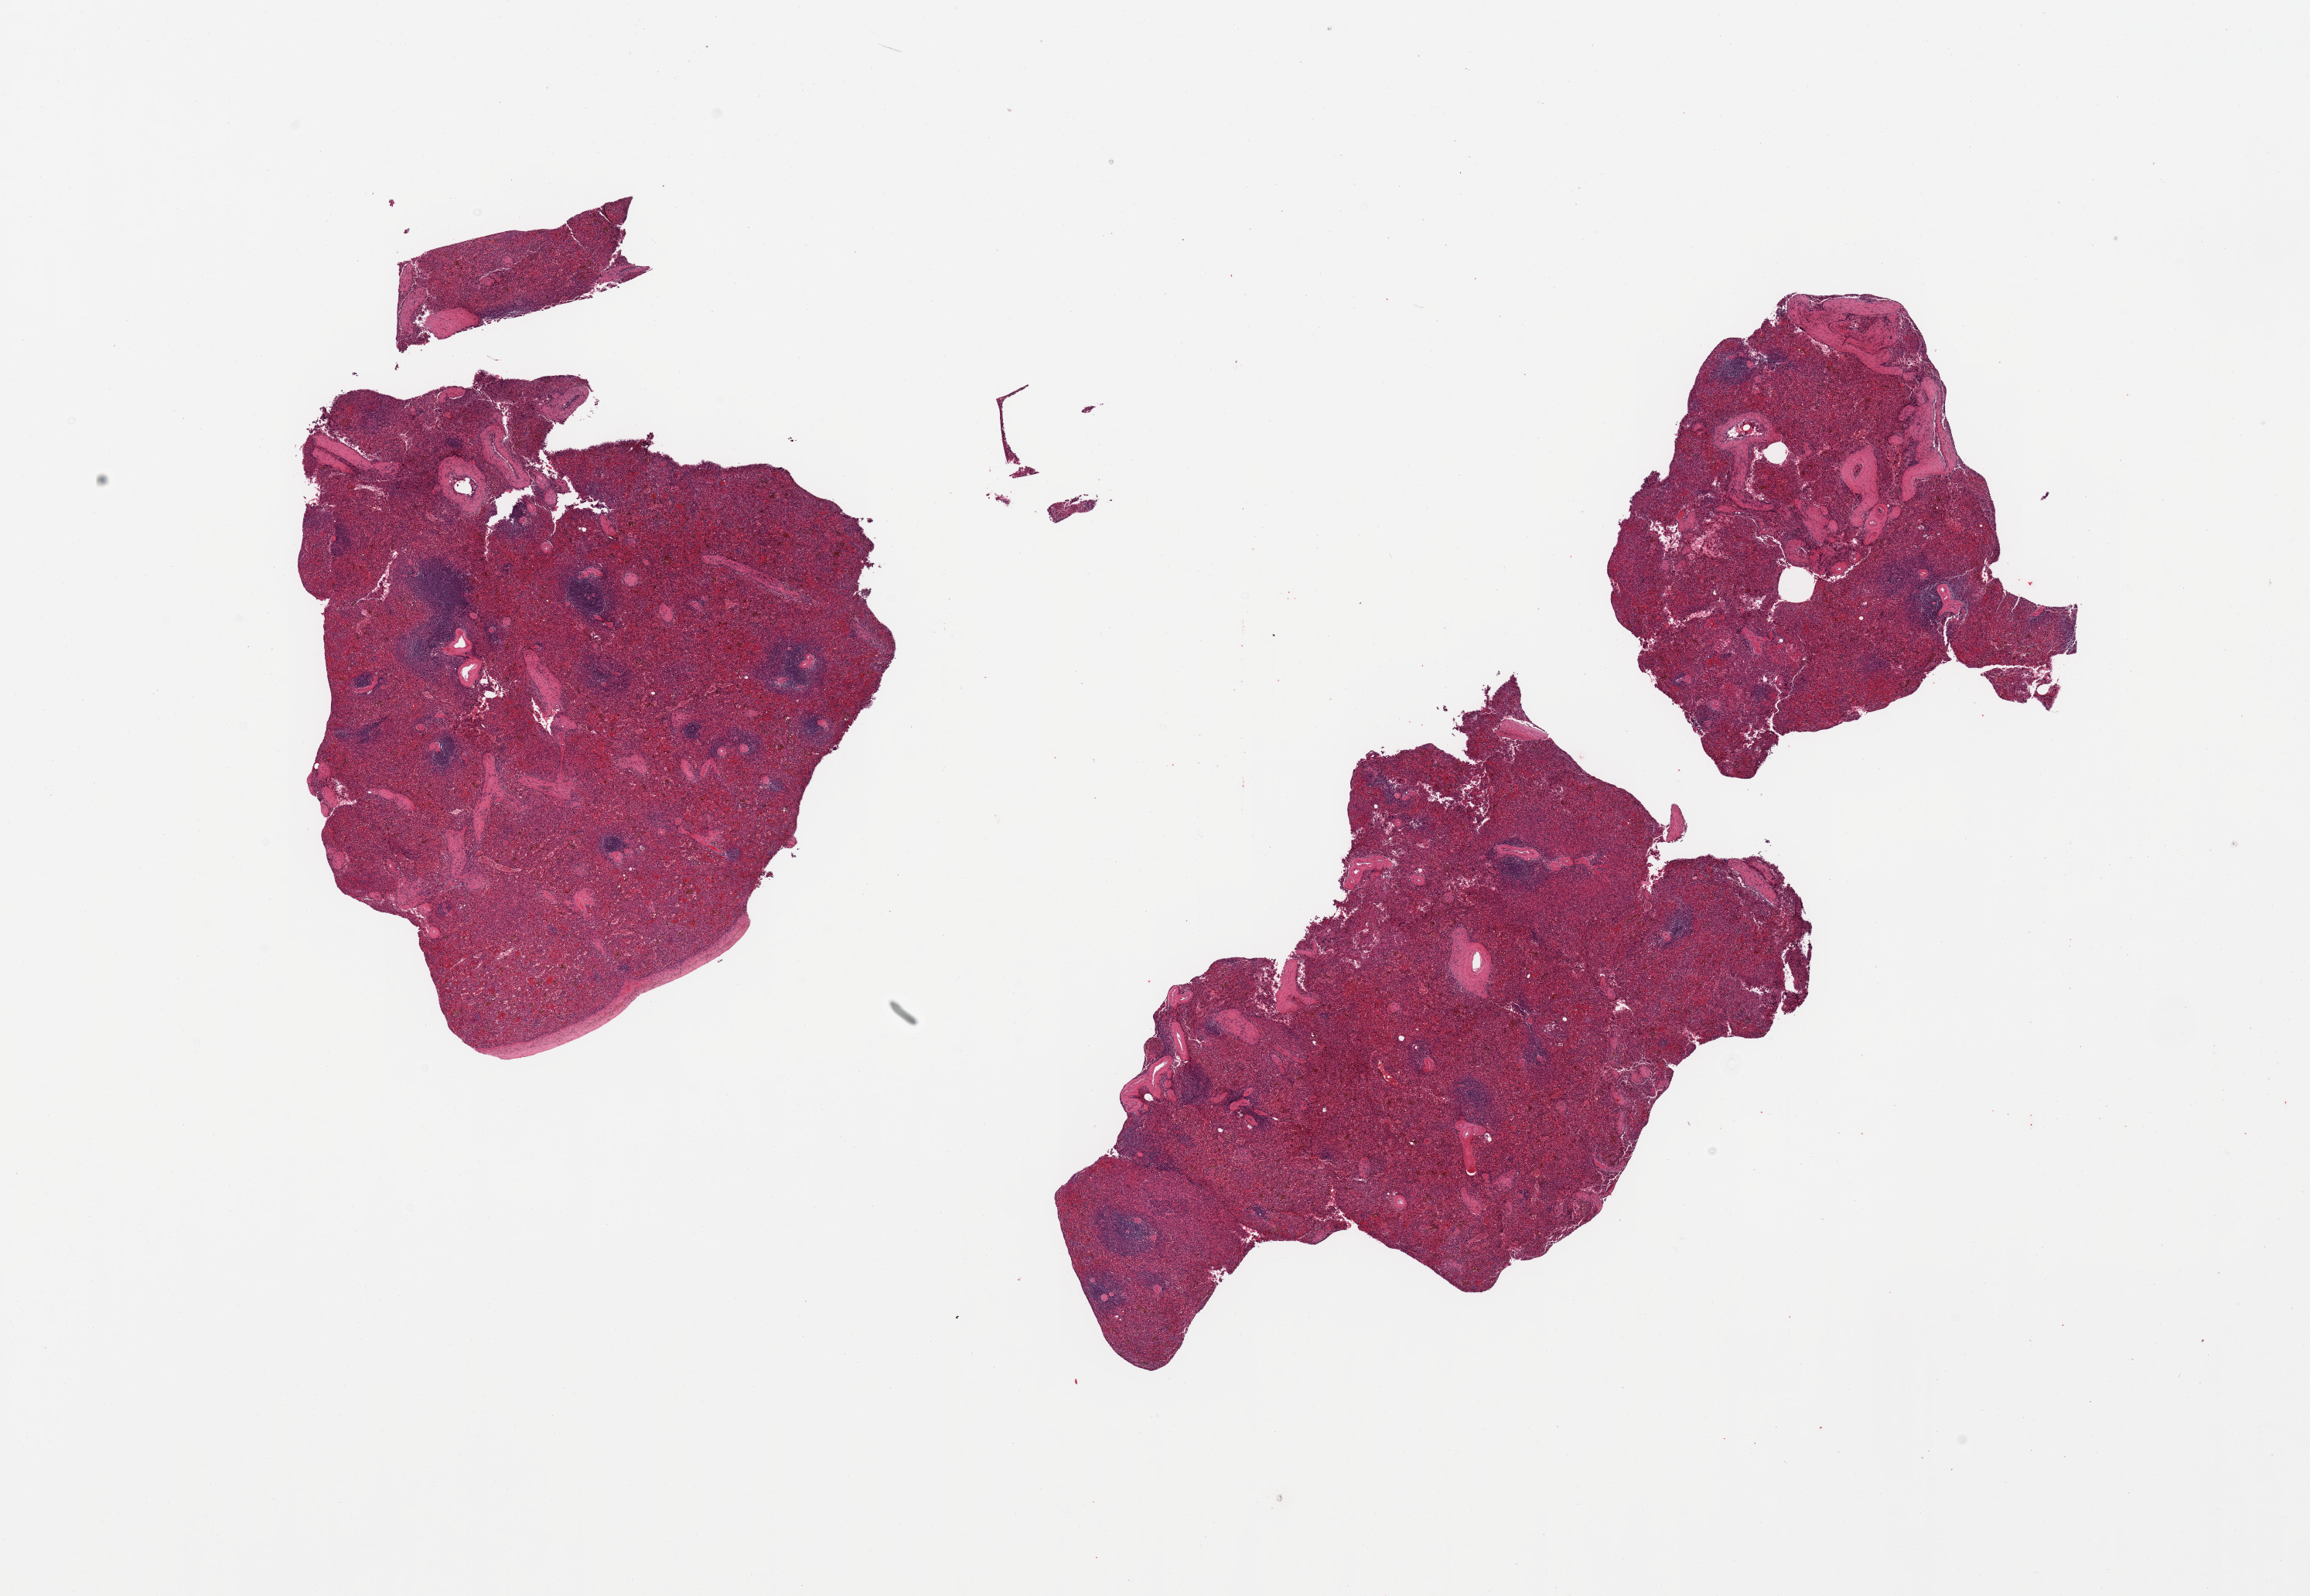
Whole-slide image, hematoxylin and eosin (H&E) stain — low-resolution overview of the scanned area, about 23.6 x 16.3 mm (slide scanned at 20x); PAXgene-fixed paraffin-embedded (PFPE) section; sampled site (target tissue): spleen; donor tissue sample. Male donor.
Pathologist's review note for this sample: 2 pieces, fragmented; congestion, portion of capsule in 1 piece.